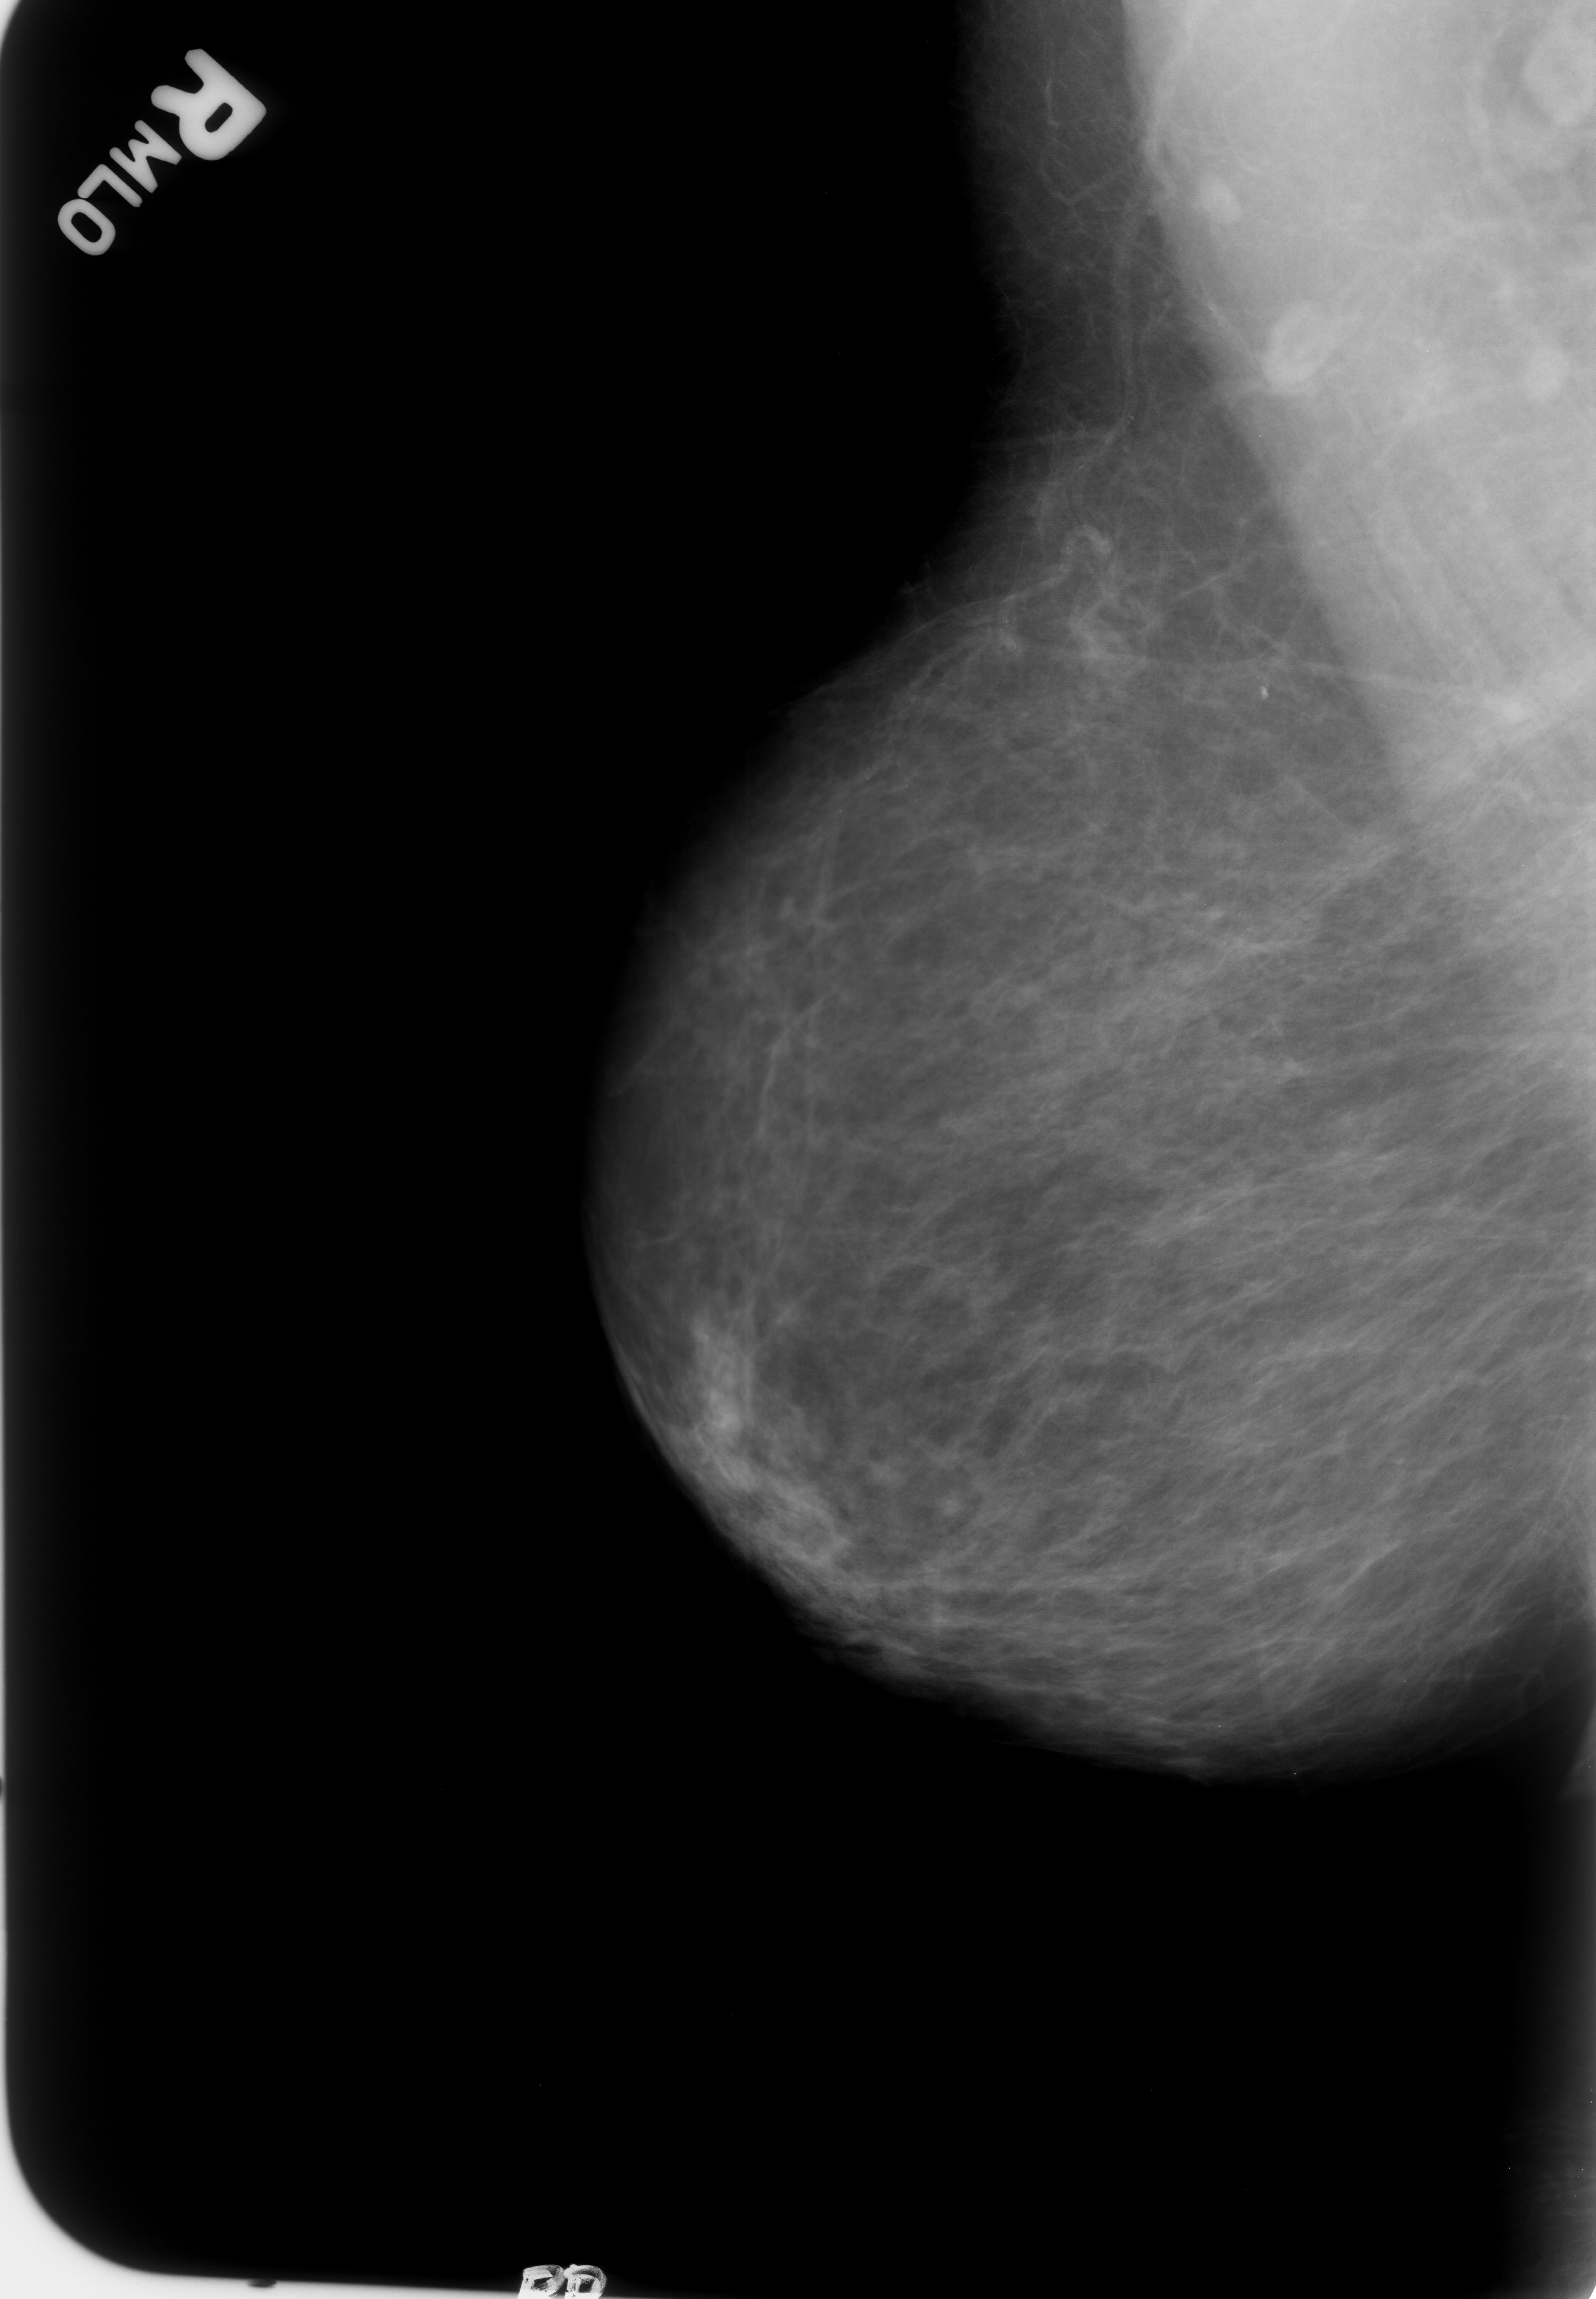
Scanned film-screen mammogram; right breast; MLO view; breast composition: almost entirely fatty (BI-RADS density category 1 of 4).
Radiologist-marked abnormalities on this image: Finding 1 of 3: mass, shape oval / lymph node, margins circumscribed; BI-RADS assessment category 2; subtlety rating 4 on a 1 (subtle) to 5 (obvious) scale; benign without callback (not worked up further). Finding 2 of 3: mass, shape oval / lymph node, margins circumscribed; BI-RADS assessment category 2; benign; no additional work-up was recommended (benign without callback). Finding 3 of 3: mass, shape oval / lymph node, margins circumscribed; BI-RADS assessment category 2; benign; no additional work-up was recommended (benign without callback).